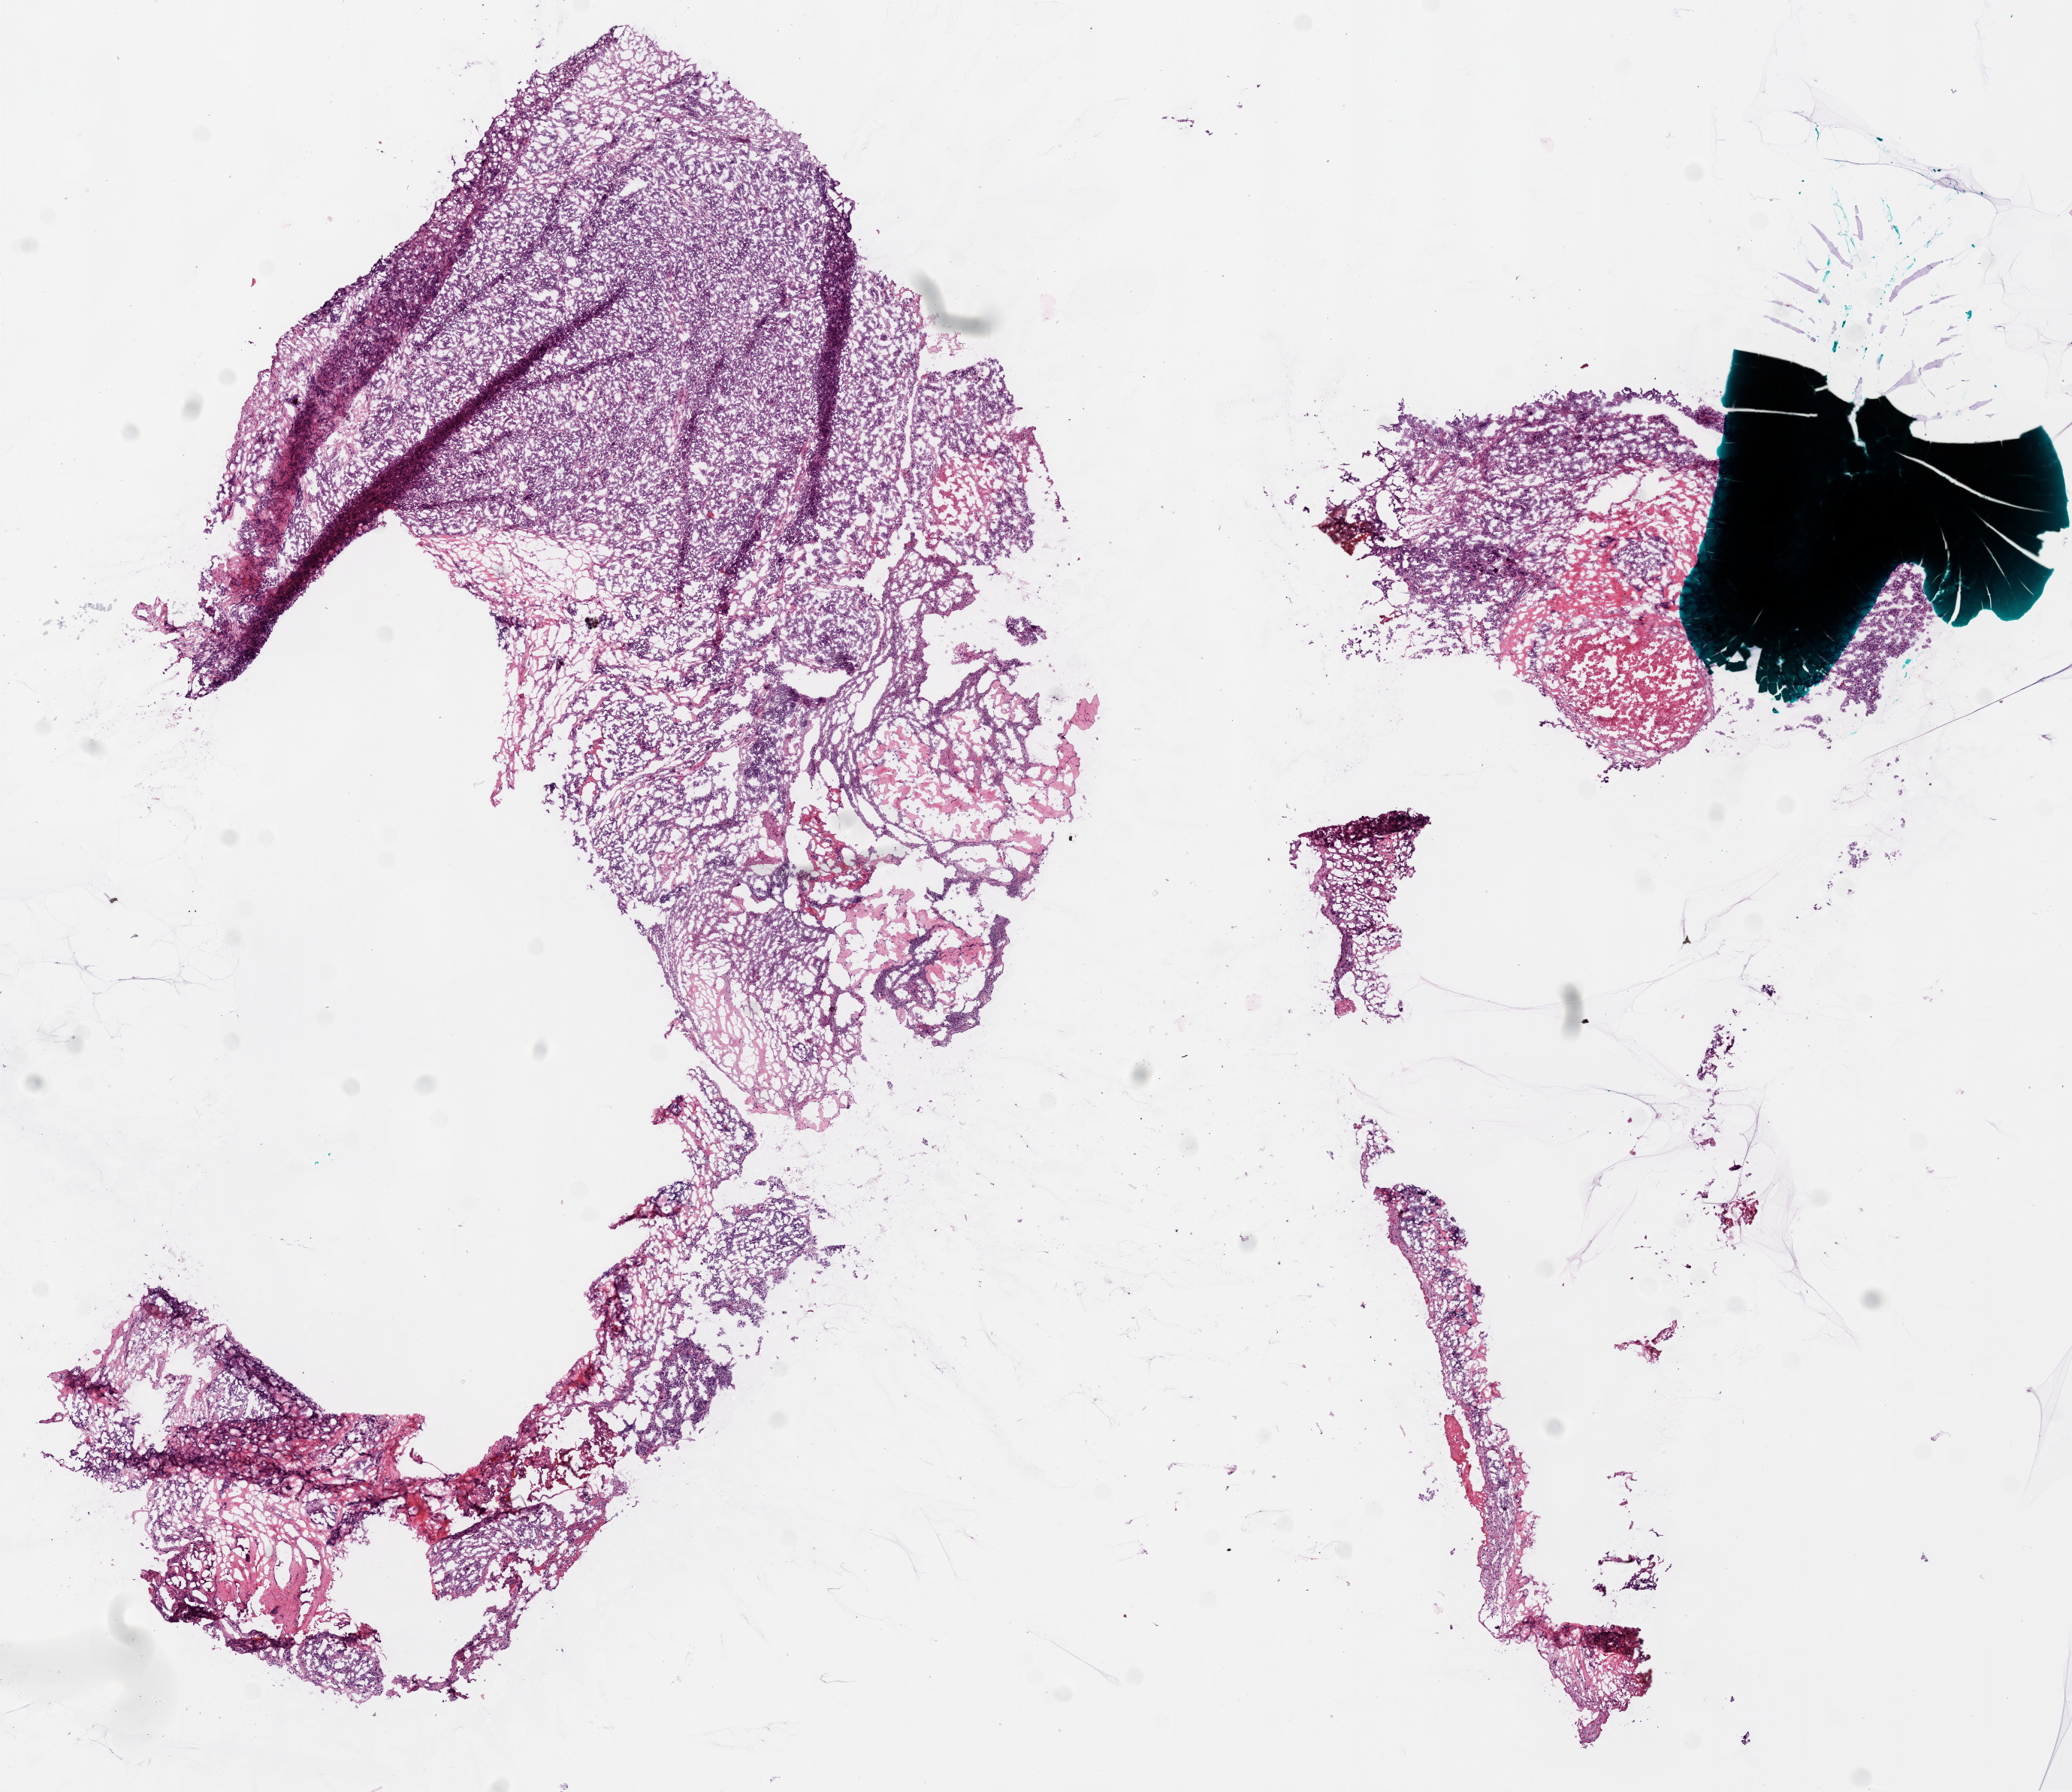
Whole-slide histology image, H&E-stained, low-resolution overview of the scanned area, about 11.1 x 9.6 mm. Frozen section from the bottom of the tissue portion. Sample: primary tumour, ovary. Female patient; age at initial diagnosis 72 years. Histologic grade: G3 (poorly differentiated). Pathologist review of this section (percent, as recorded): tumour cells 80%, tumour nuclei 88%, normal cells 0%, stromal cells 16%, necrosis 4%.
- FIGO stage: IV
- pathologic diagnosis: Serous cystadenocarcinoma, NOS